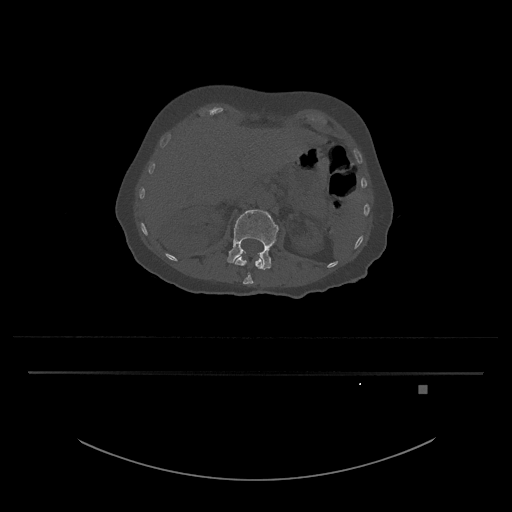
CT including the spine, one axial slice; reconstruction kernel Br40s/3; 120 kVp; bone window (W 1800 / L 400 HU); 0.5 mm slice thickness; 512 × 512 image matrix, field of view 500 × 500 mm. Patient: female, 57 years. Case-level facts recorded for this patient, not image findings: primary cancer: cervical.
Structures marked on this image (semi-automatic segmentation, software-assisted and operator-edited):
- L1 vertebra: bounding box [x1, y1, x2, y2] px = [235, 253, 263, 285]